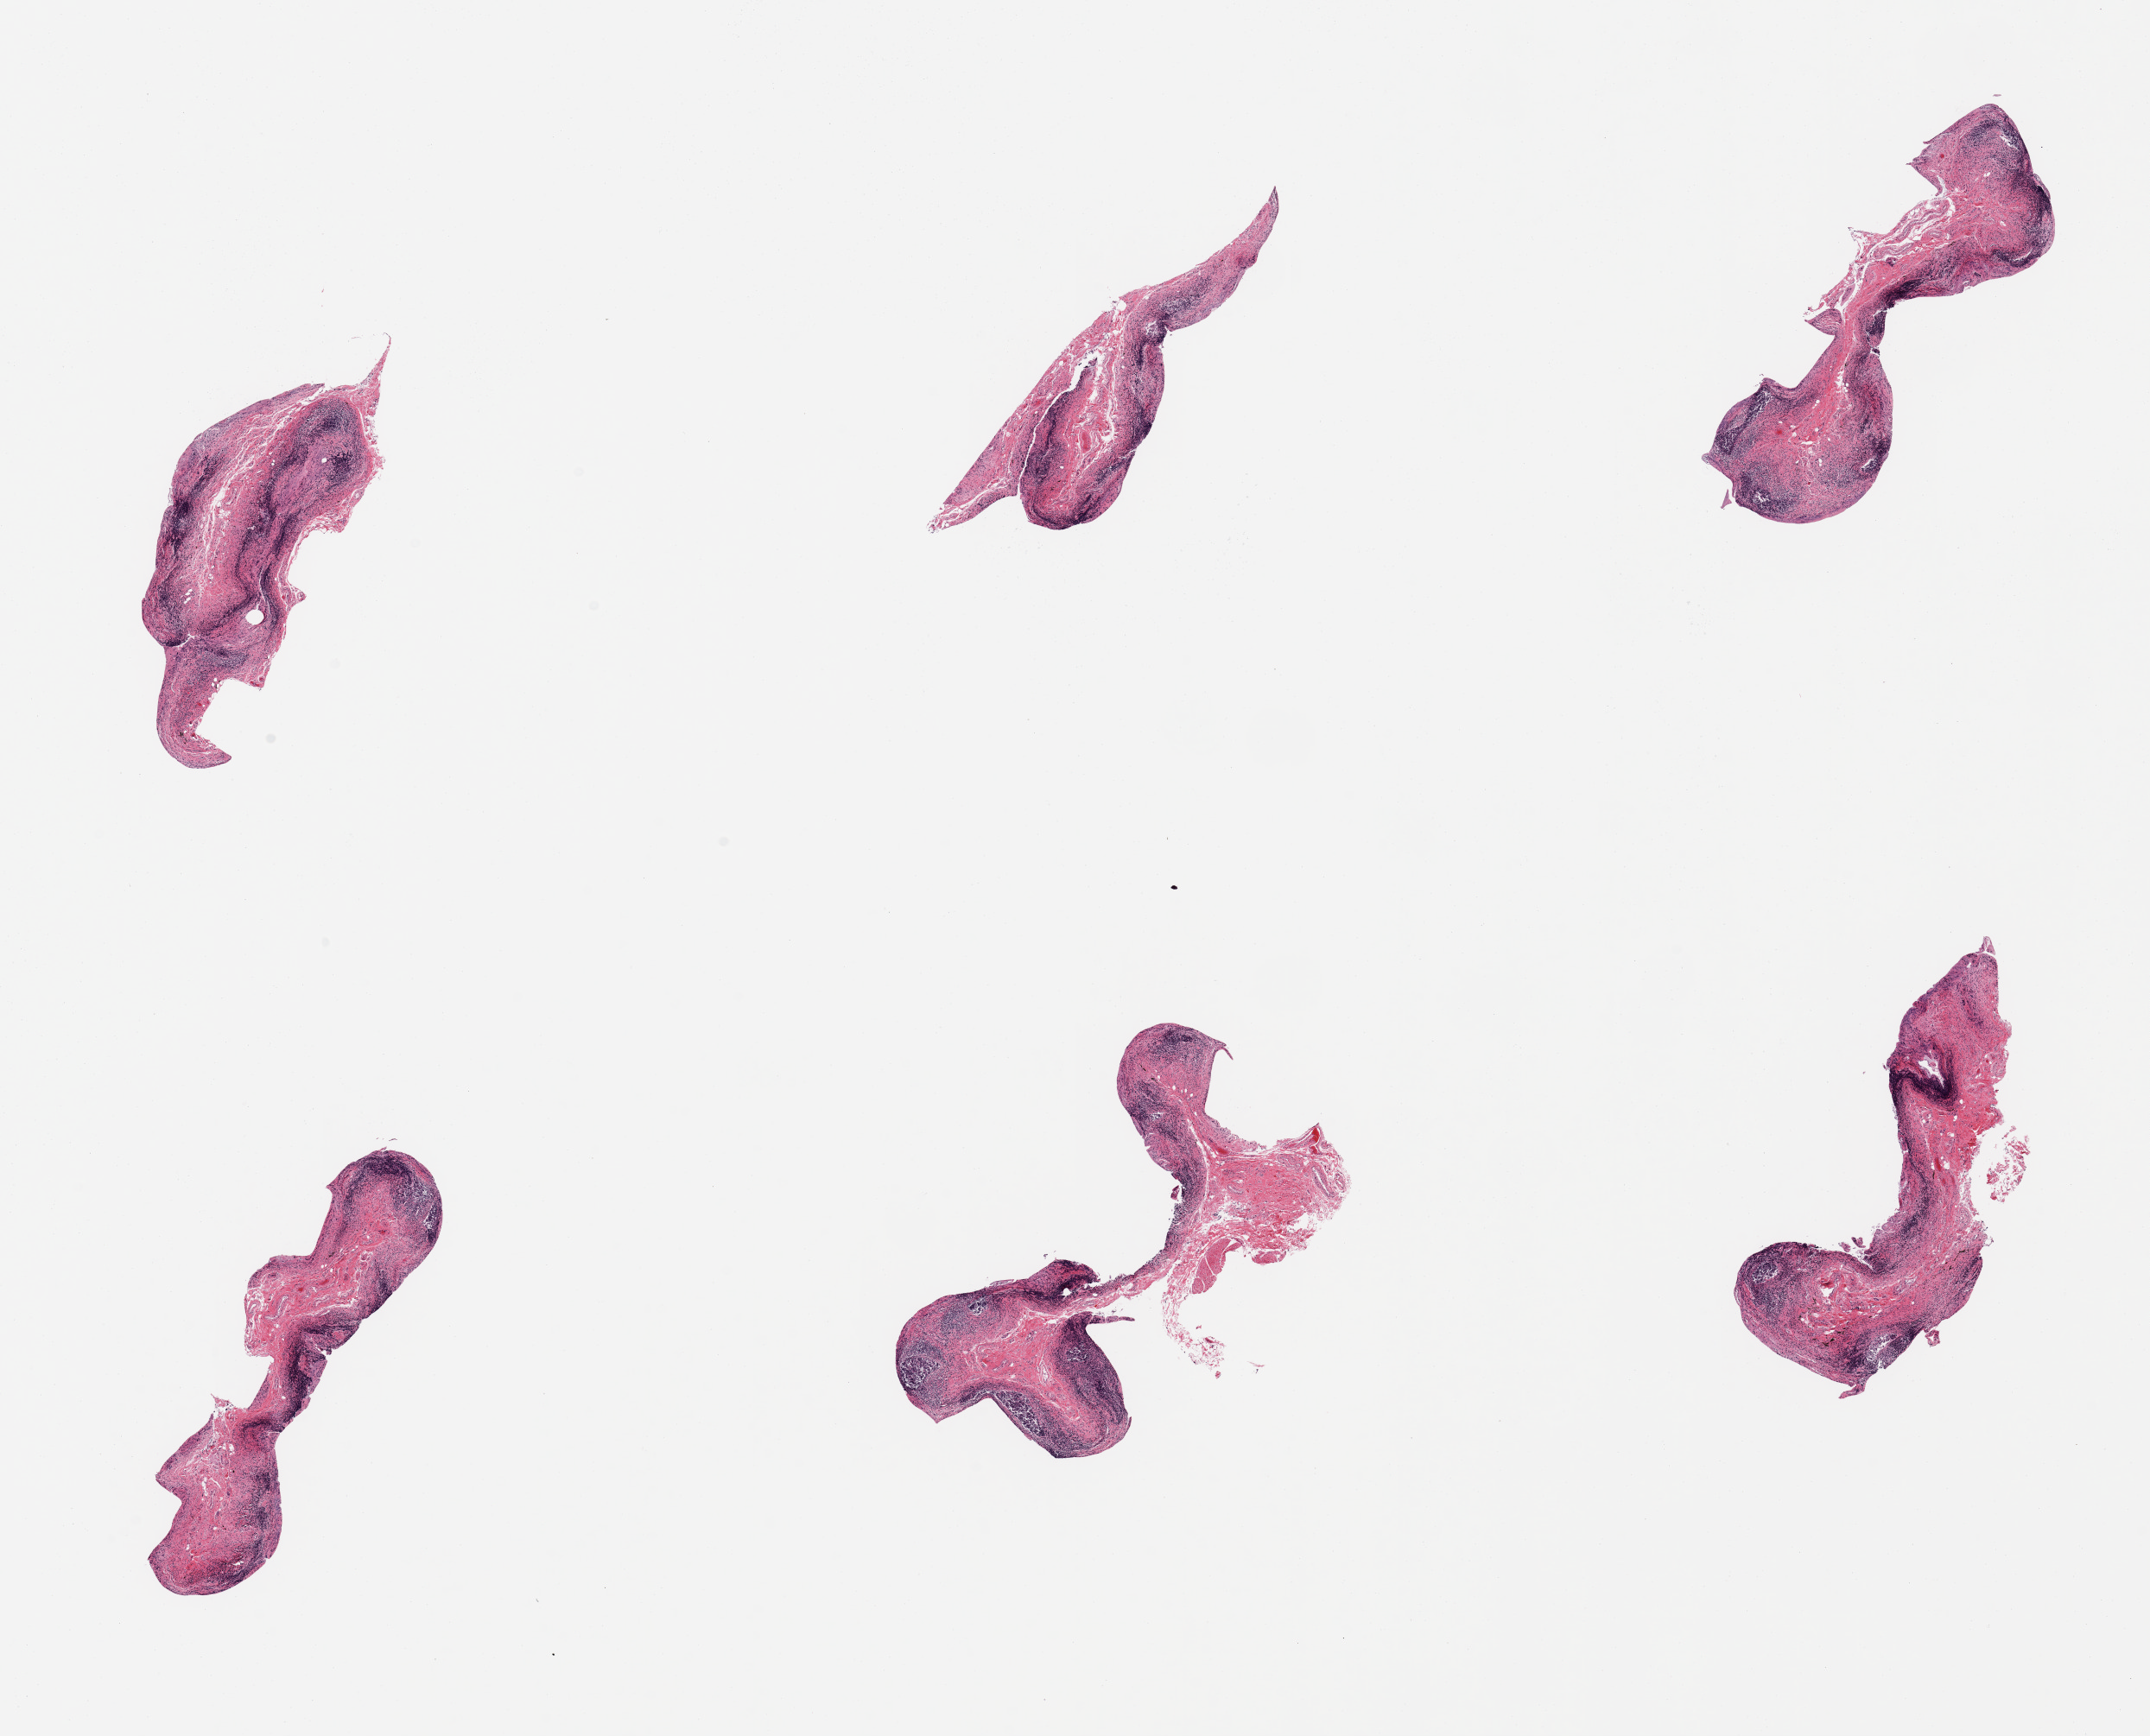
Hematoxylin and eosin (H&E) whole-slide image, low-resolution overview of the scanned area, about 19.7 x 15.9 mm (from a 20x scan); PAXgene-fixed paraffin-embedded (PFPE) section; target tissue: ileum; tissue donor sample. Donor: female.
Reviewer comment on this tissue sample: 6 pieces; mucosa autolyzed but thin layer of lymphoid cells present on all pieces.